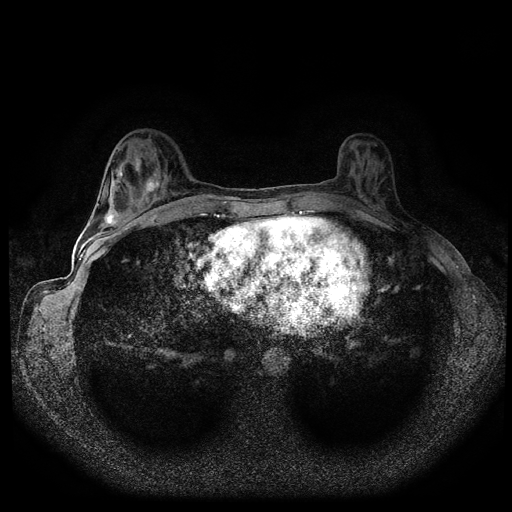
Breast MRI (dynamic contrast-enhanced, multi-phase), one axial slice. Slice 36 of 108 in the series (ordered by position). Dynamic contrast-enhanced series, time point 2 of 5 at this slice position (early post-contrast). 1.5 T. TE 2.7 ms, TR 5.5 ms. 512 × 512 image matrix. Patient: female, 36 years.
Annotated regions visible in this slice (semi-automatically segmented with operator editing):
- breast lesion (labelled benign in the annotation): bounding box [x1, y1, x2, y2] px = [144, 175, 161, 195]
- breast lesion (labelled benign in the annotation): [102, 207, 121, 227]